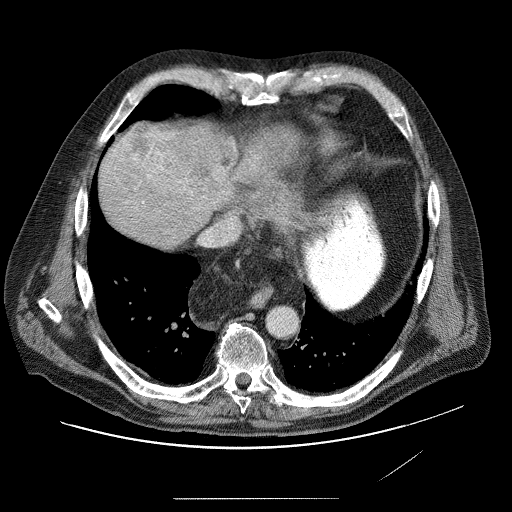
Contrast-enhanced abdominal CT (liver protocol), one axial slice; slice 74 of 89 in the series (ordered by position); reconstruction kernel STANDARD; 120 kVp; soft-tissue window (W 400 / L 40 HU); 2.5 mm slice thickness; 512 × 512 image matrix. Case-level facts recorded for this patient, not image findings: diagnosis: hepatocellular carcinoma (patient treated with transarterial chemoembolisation; whether this scan precedes or follows treatment is not stated here); TNM stage (as recorded): Stage-IVA; Child-Pugh class: A; tumour nodularity: multinodular.
Structures marked on this image (semi-automatically segmented with operator editing):
- liver parenchyma outside the tumour (the mass and vessels are separate outlines, so this box may not span the whole liver): bounding box [x1, y1, x2, y2] px = [102, 124, 240, 238]
- mass: [125, 125, 286, 236]
- liver vessels: [129, 180, 239, 227]